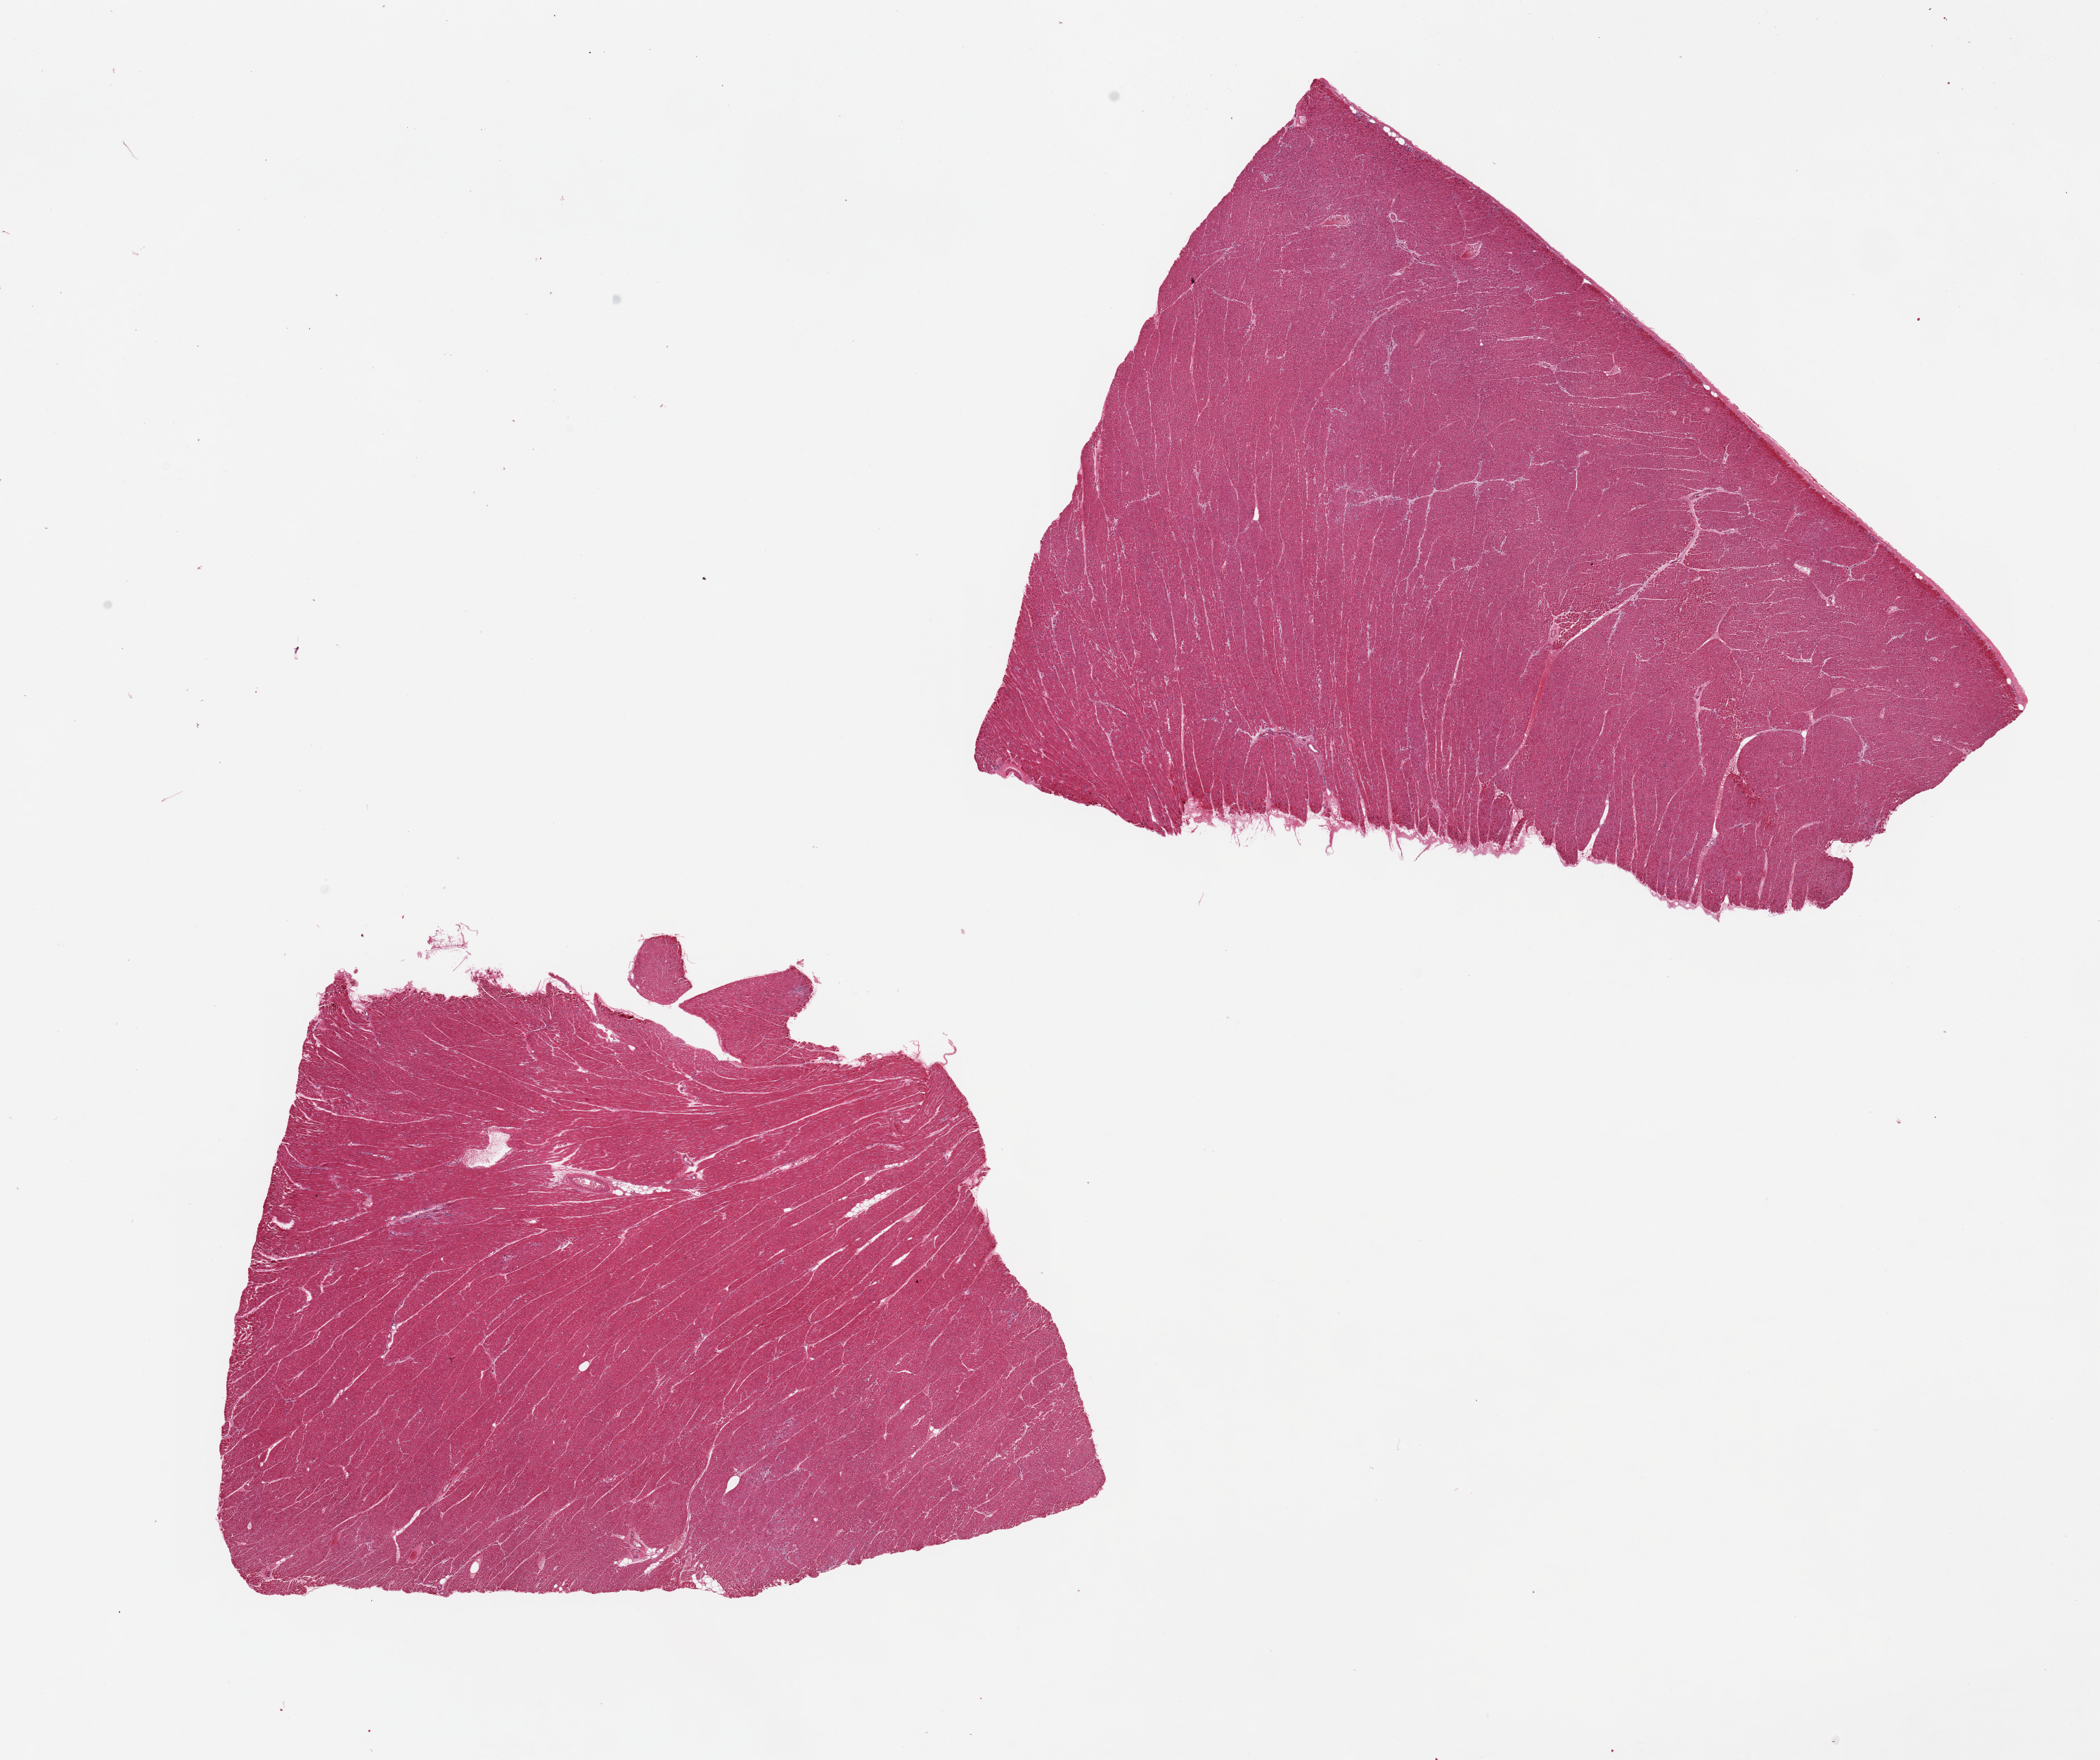
Whole-slide image, hematoxylin and eosin (H&E) stain — low-resolution overview of the scanned area, about 23.6 x 19.8 mm (acquisition: 20x scan). PAXgene-fixed, paraffin-embedded tissue. Sampled site (target tissue): heart. Donor tissue sample. Donor sex: female.
Reviewer comment on this tissue sample: 2 pieces. Contraction bands.